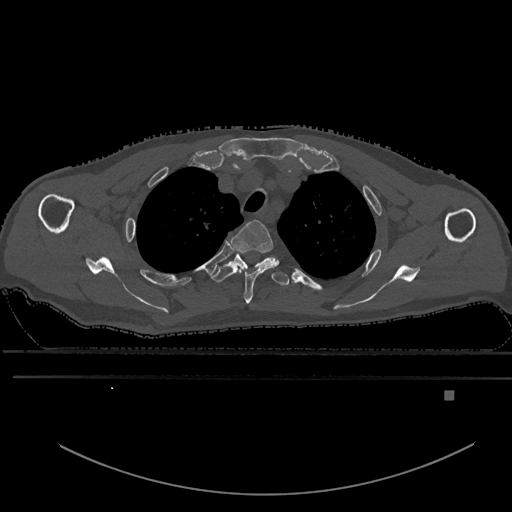
CT including the spine, one axial slice. Slice 475 of 969 in the series (ordered by position). Bone window (W 1800 / L 400 HU). 0.5 mm slice thickness. 512 × 512 image matrix. Male patient, age 82 years. From the clinical record (not read from this slice): primary cancer: prostate.
Annotated regions visible in this slice (semi-automatic segmentation, software-assisted and operator-edited):
- T2 vertebra: bounding box <231,220,279,304> (left, top, right, bottom; pixels)
- T3 vertebra: <211,251,289,286>